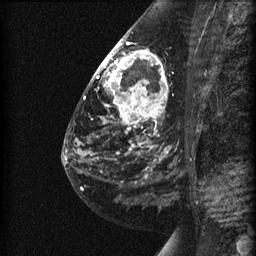
Breast MRI (dynamic contrast-enhanced), one sagittal slice. Dynamic contrast-enhanced series, image 2 of 3 at this slice position (ordered by acquisition). 1.5 T. TE 4.2 ms, TR 22.7 ms. 1.5 mm slice thickness. 256 × 256 image matrix, field of view 180 × 180 mm. Patient: female, 48 years. Case-level facts recorded for this patient, not image findings: setting: breast cancer imaged before/during neoadjuvant chemotherapy; receptor status: triple-negative.
Annotated regions visible in this slice (semi-automatic segmentation, software-assisted and operator-edited):
- analysis volume of interest (the breast-tissue region the enhancement analysis was run in; not a lesion): bounding box [x1, y1, x2, y2] px = [89, 27, 190, 180]
- tumour enhancement mask (voxels above the 90 % enhancement threshold inside the analysis volume of interest): [95, 42, 166, 154]